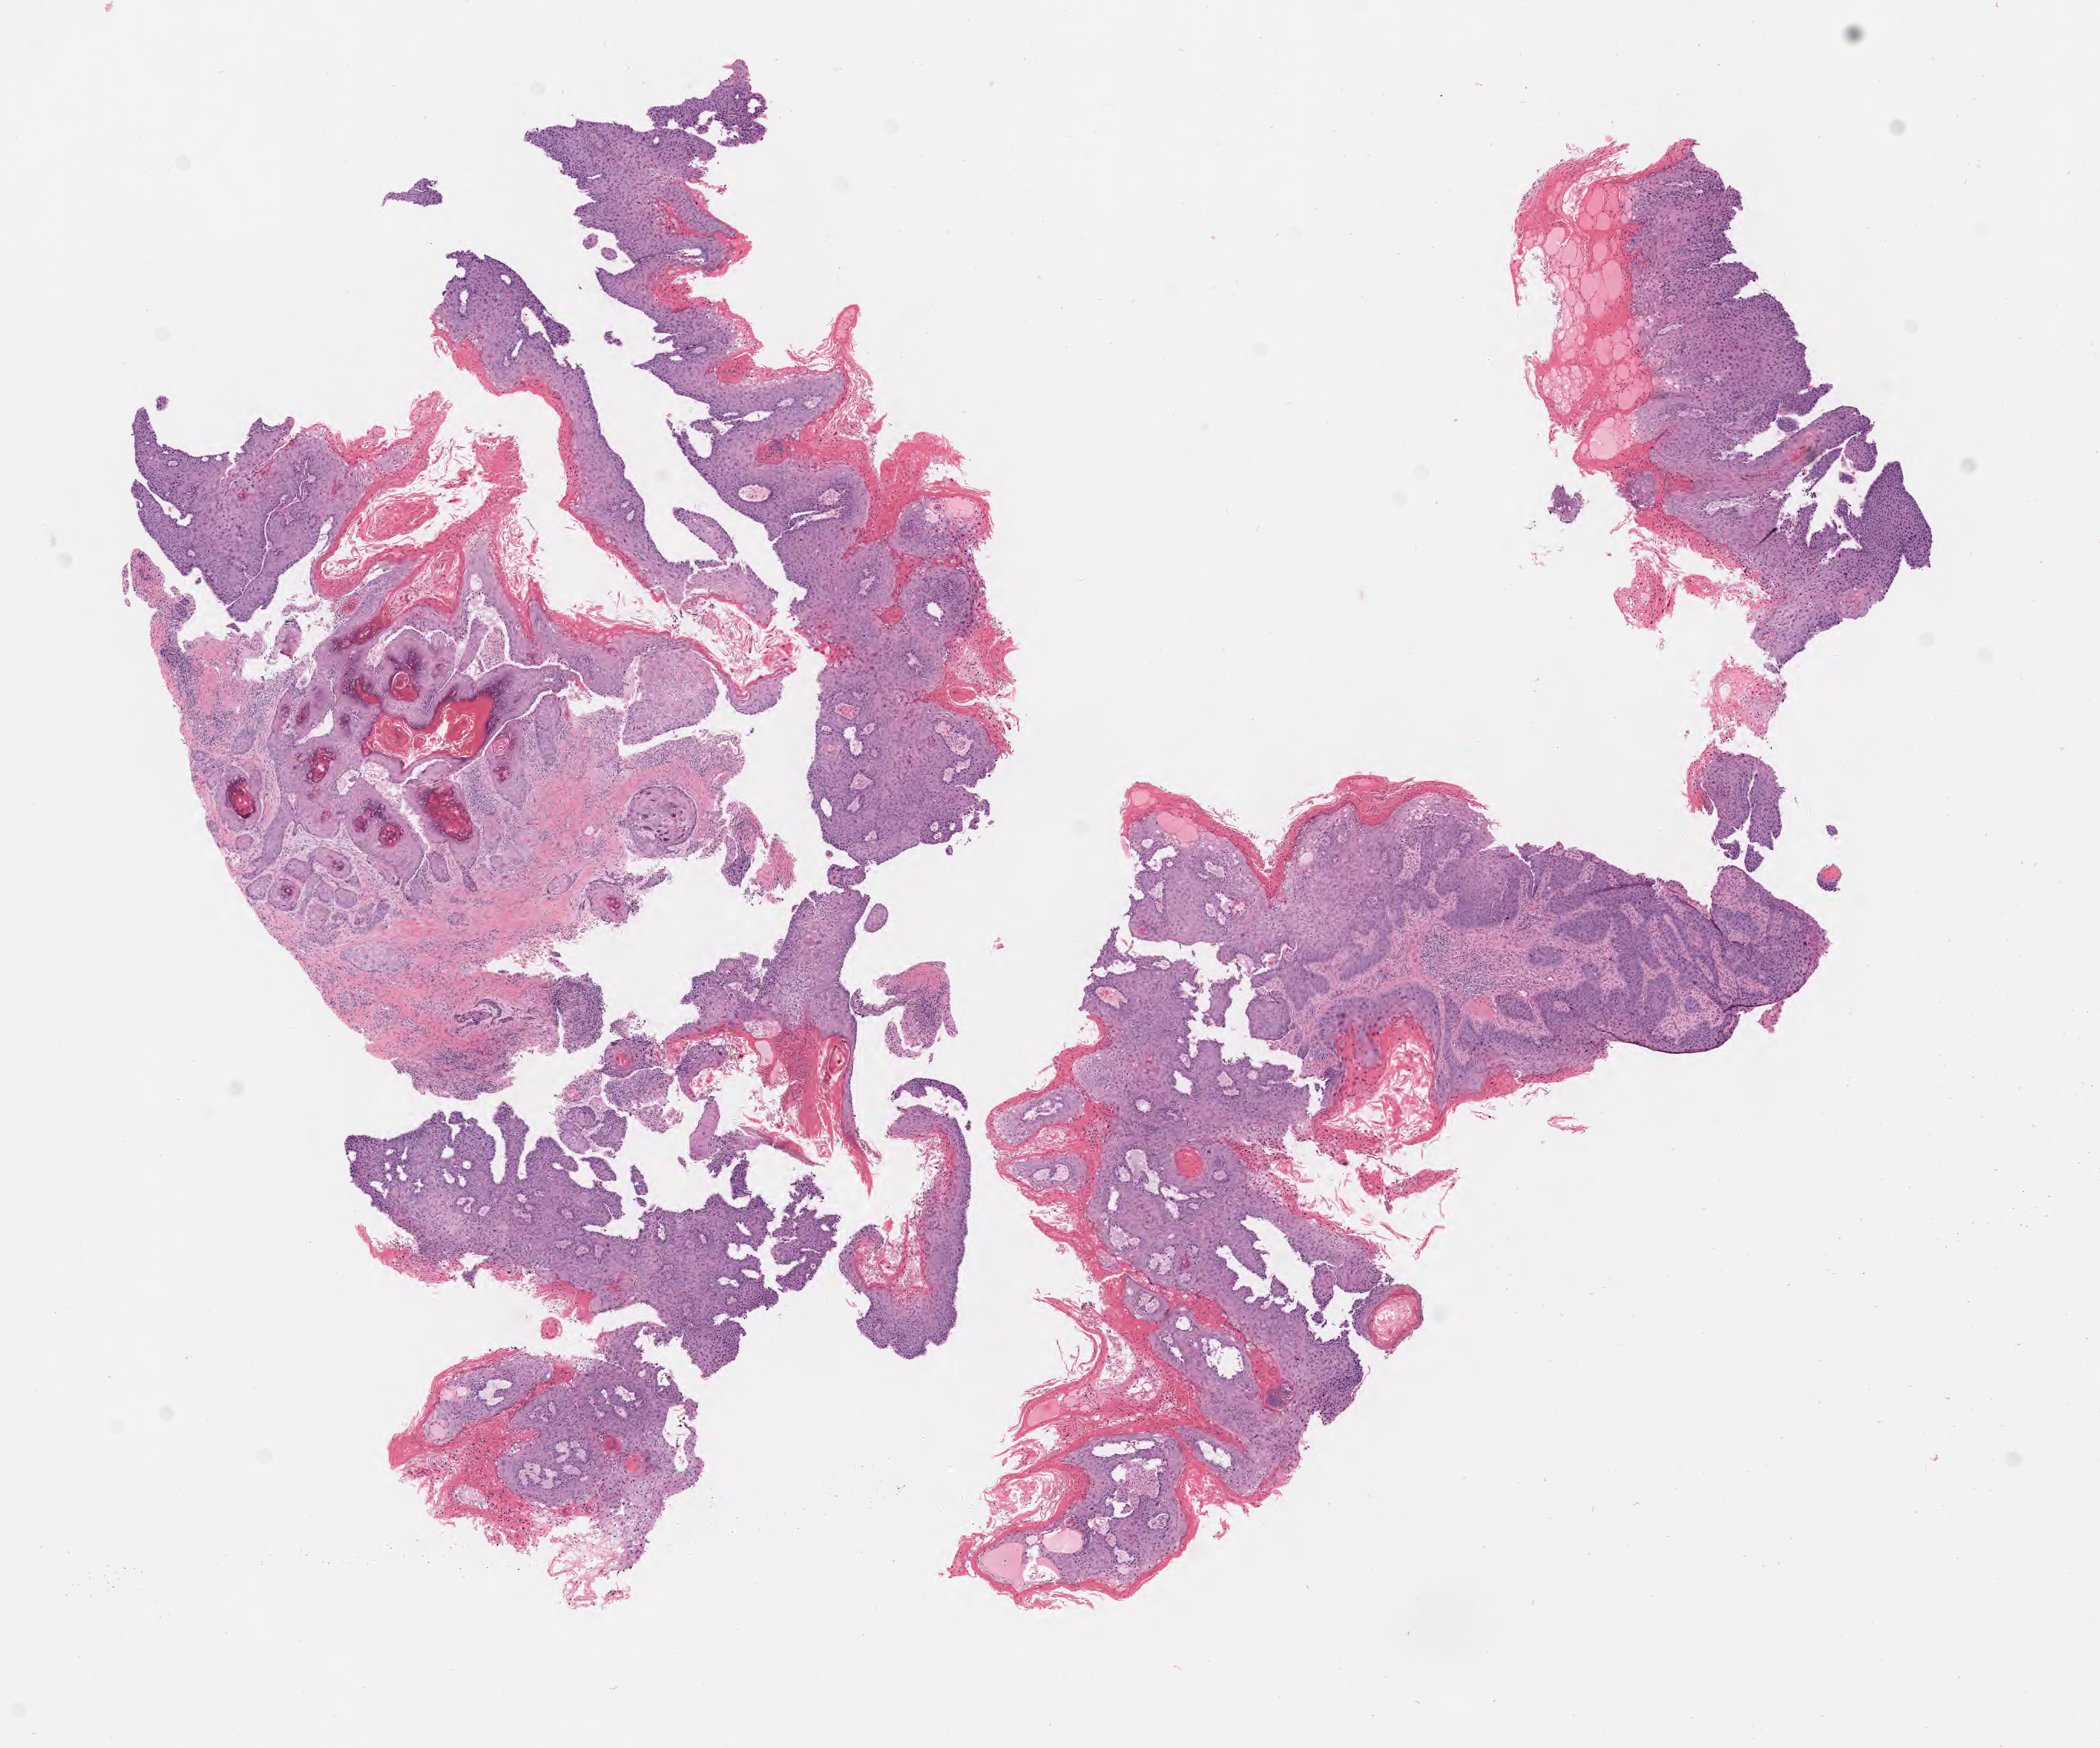
Whole-slide image, haematoxylin and eosin stain, low-resolution overview of the scanned area, about 11.1 x 9.2 mm, specimen: tumor tissue, site: cervix. Female patient, 41 years old.
• histologic diagnosis: Warty carcinoma